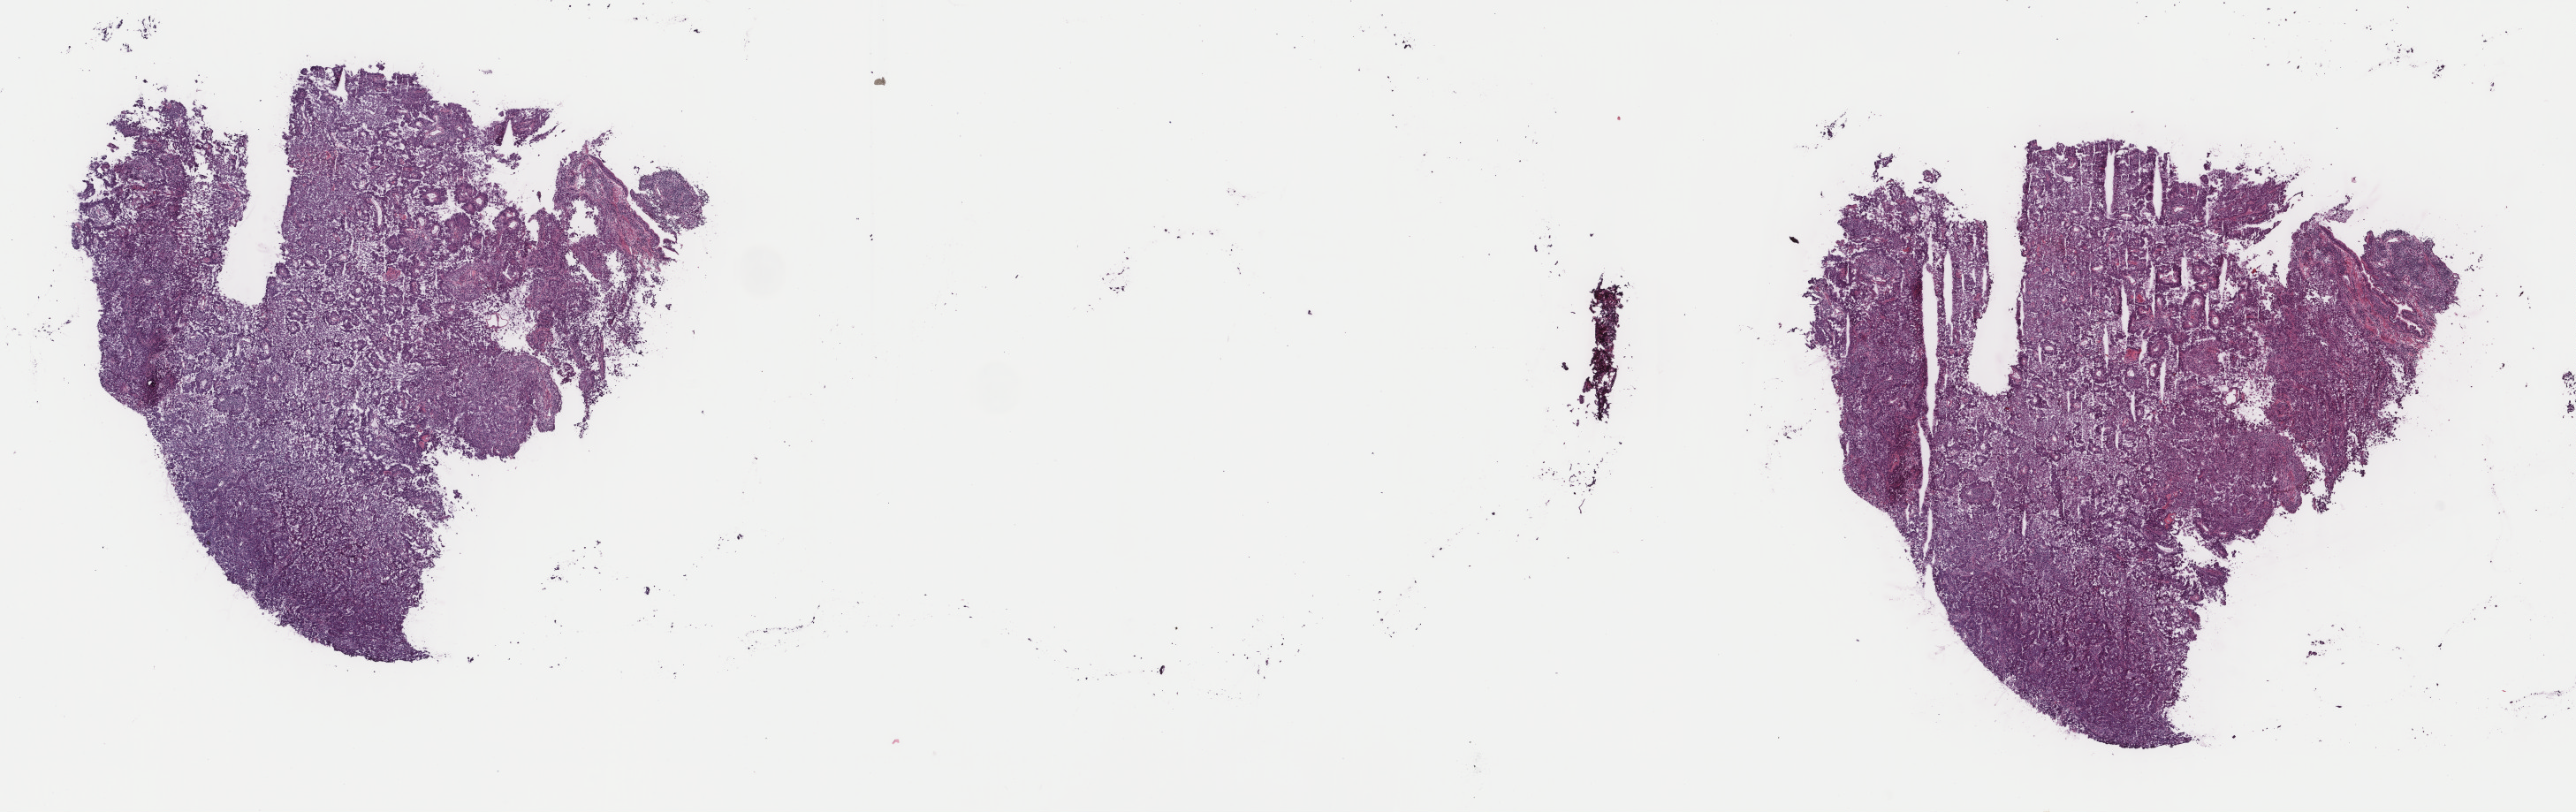
Whole-slide histology image, Hematoxylin and eosin (H&E) stained, shown as a low-resolution overview of the whole scanned area (about 23.1 x 7.3 mm). Frozen section from the top of the tissue portion. Primary tumour sample from the lung. Patient: female, age at initial diagnosis 71 years. Slide review estimates, as recorded: tumour cells 99%, tumour nuclei 65%, normal cells 0%, stromal cells 0%, necrosis 1%. Infiltration values recorded for this section: lymphocyte infiltration 15%, monocyte infiltration 1%, neutrophil infiltration 0%.
- laterality: right
- histologic diagnosis: Adenocarcinoma with mixed subtypes
- AJCC pathologic stage: IIB (6th edition)